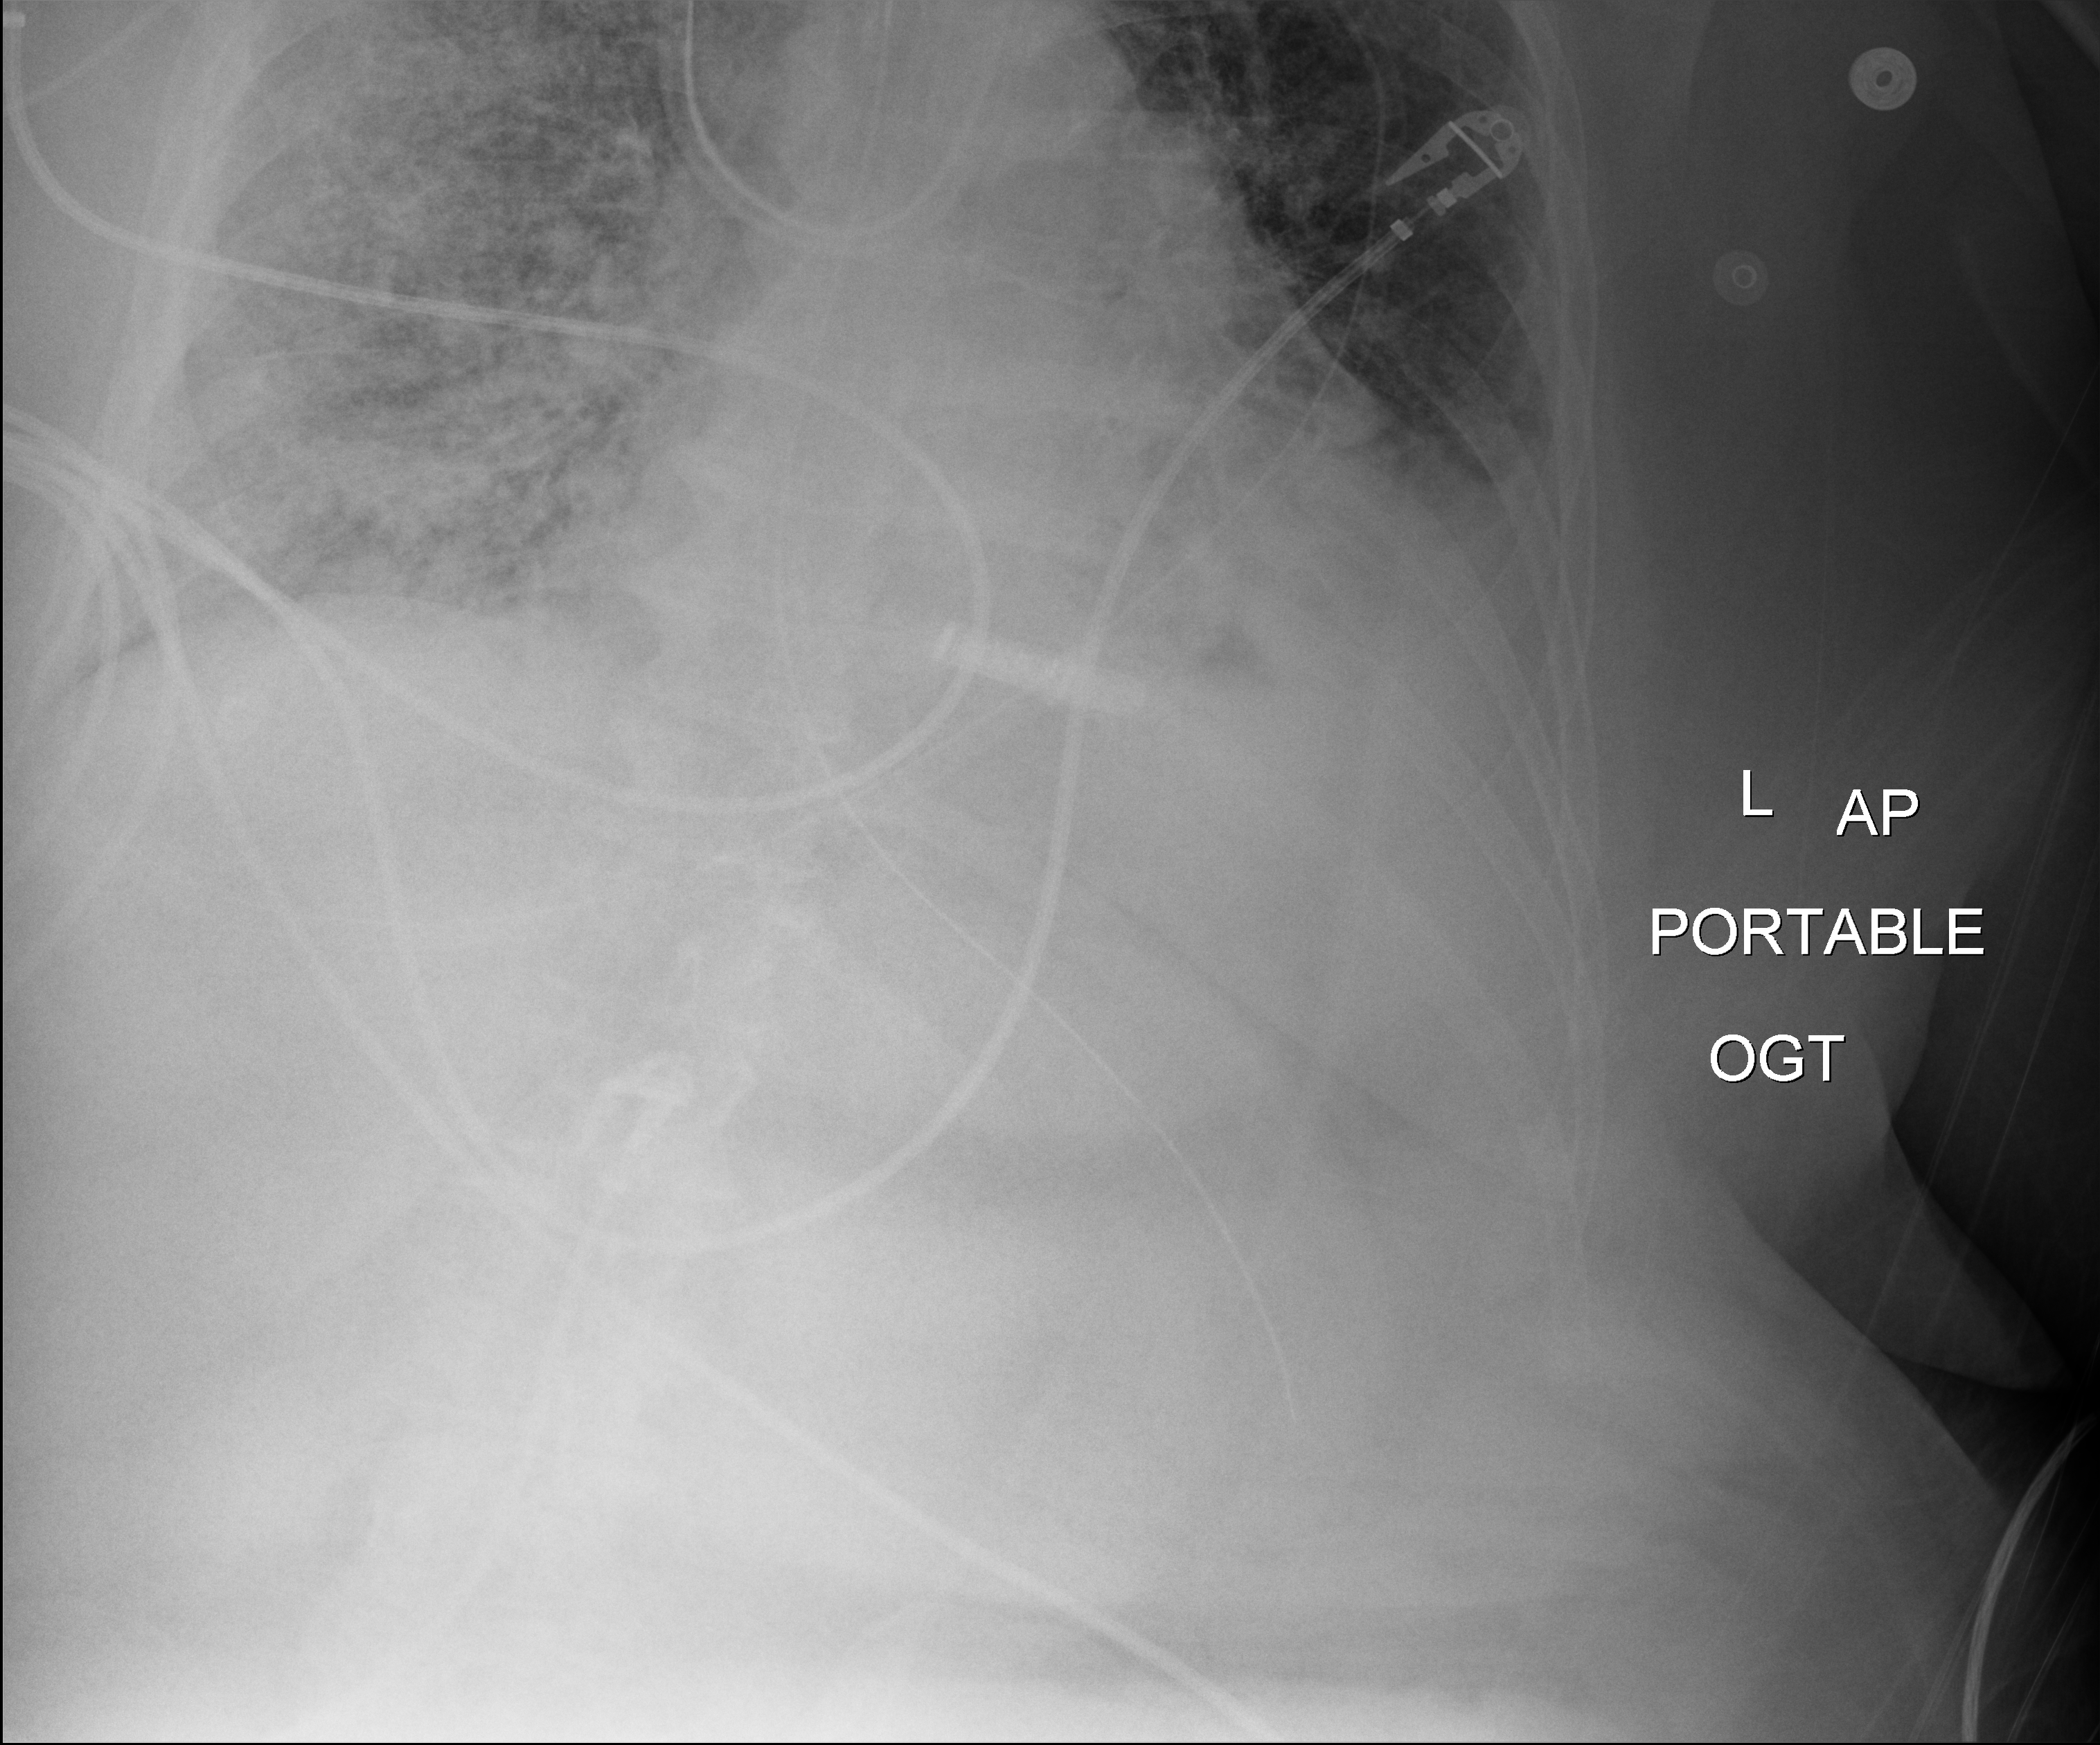
Portable chest radiograph, anteroposterior (AP) projection. Female patient hospitalised with COVID-19, age 60–74 years.
Hospital-stay facts (about this admission, not read from this image; timing relative to this image not recorded): length of hospital stay: 28 days; mechanically ventilated during this hospital stay: yes.